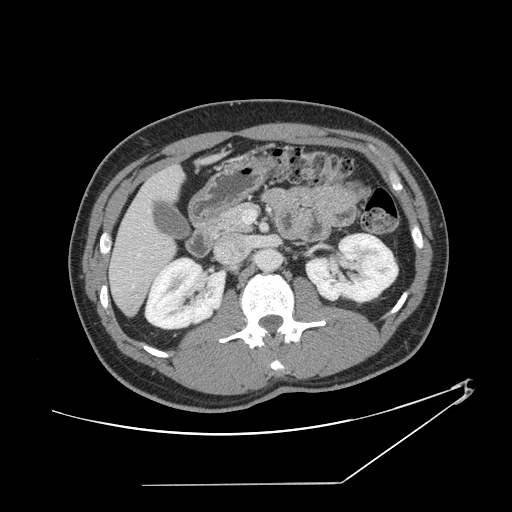
Contrast-enhanced abdominal CT, one axial slice. Reconstruction kernel STANDARD. 120 kVp. Intravenous contrast given. Soft-tissue window (W 400 / L 40 HU). 2.5 mm slice thickness. 512 × 512 image matrix, field of view 432 × 432 mm. Male patient, age 45 years. From the clinical record (not read from this slice): diagnosis: colorectal cancer liver metastases, imaged before liver resection; multiple liver metastases: no; largest metastasis: 1 cm.
Structures marked on this image (manually delineated by an expert):
- hepatic veins: bounding box [x1, y1, x2, y2] px = [137, 210, 149, 258]
- liver: [110, 168, 182, 314]
- planned liver remnant (the part of the liver to remain after resection): [110, 168, 181, 314]
- portal vein (with intrahepatic branches): [242, 211, 256, 224]